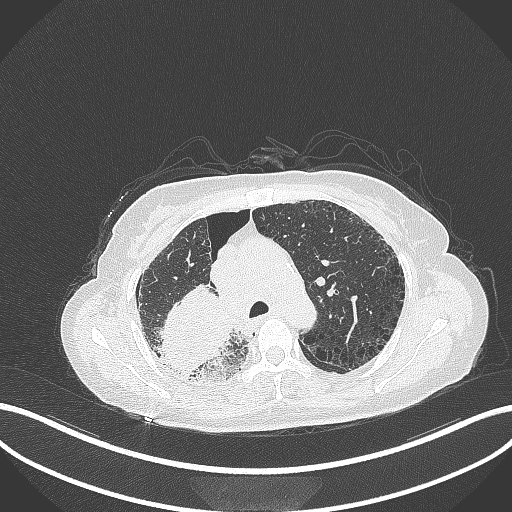
Chest CT, one axial slice; slice 244 of 408 in the series (ordered by position); reconstruction kernel B70f; lung window (W 1500 / L -600 HU); 512 × 512 image matrix, field of view 400 × 400 mm. Female patient, age 64 years. From the clinical record (not read from this slice): clinical TNM (as recorded): T3 N3 M0.
Structures marked on this image (bounding box drawn by a radiologist):
- lung tumour (recorded histology: squamous cell carcinoma): bounding box (x1, y1, x2, y2) in pixels: (158, 281, 233, 372)